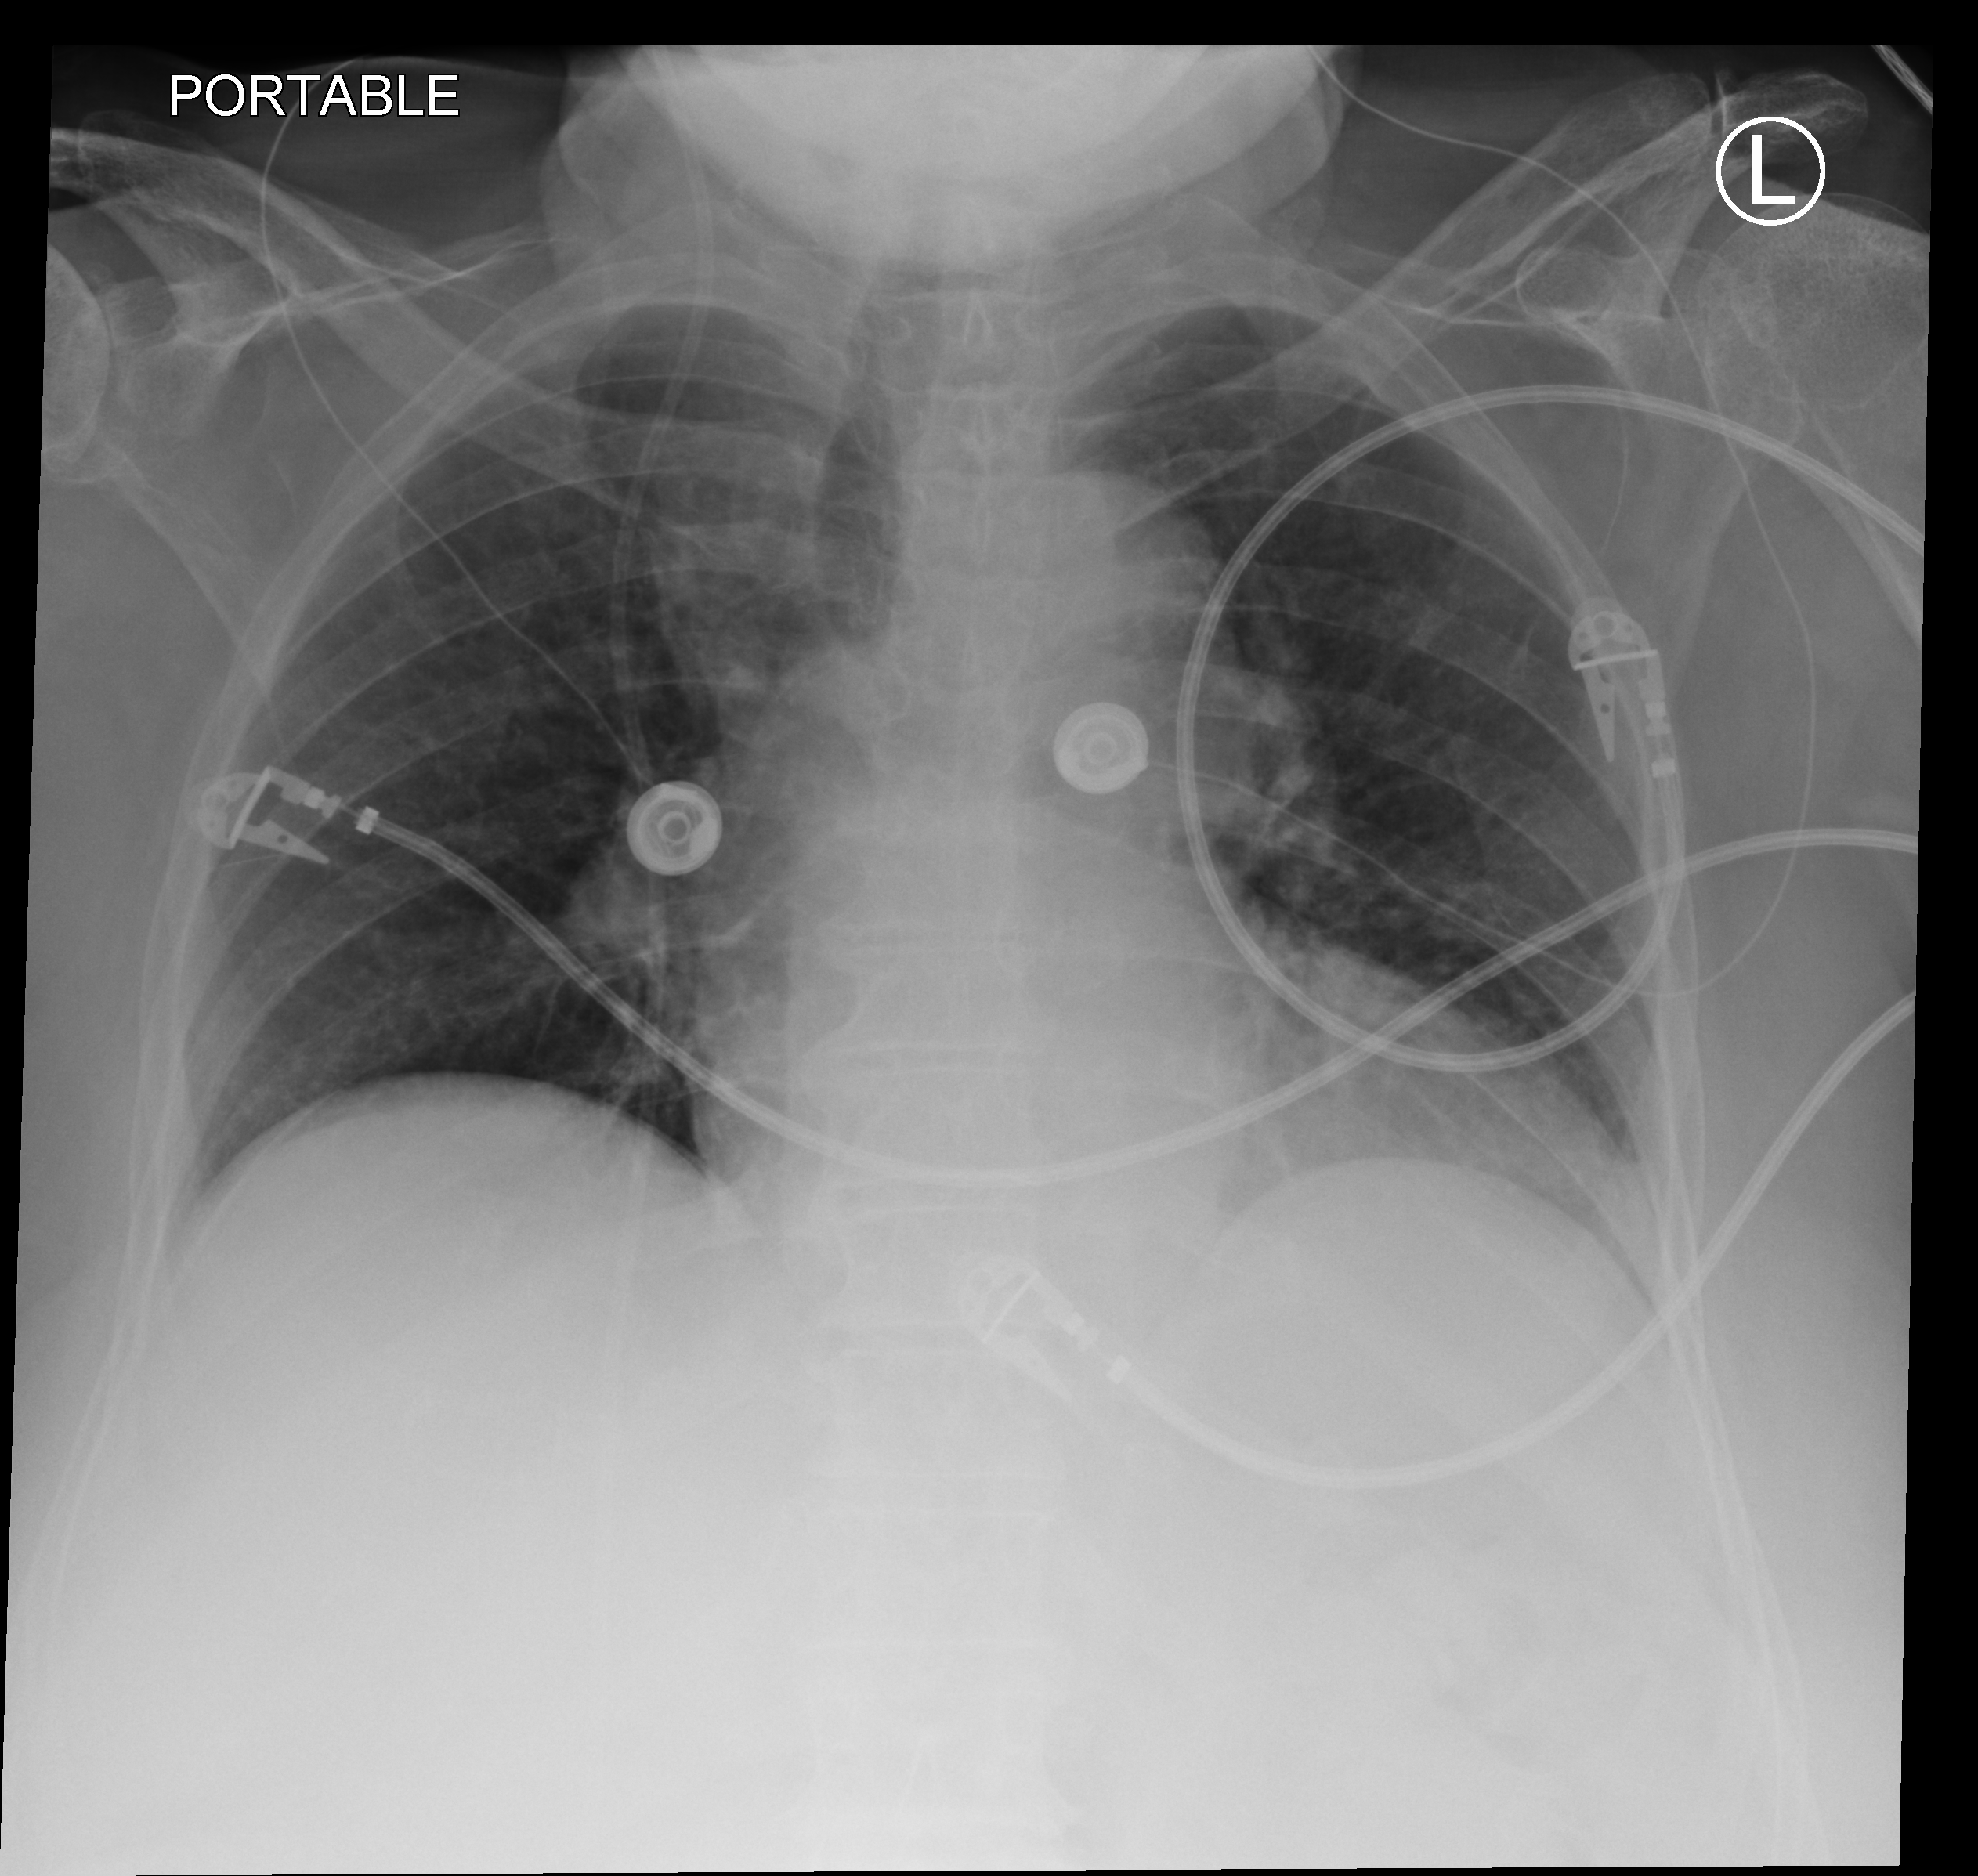
Bedside chest radiograph (computed radiography), anteroposterior (AP) projection. Patient hospitalised with COVID-19; female, aged 75–90 years.
From the hospital-stay record, not from the radiograph (when in the stay this image was taken is not recorded):
- admitted to intensive care during this hospital stay: yes